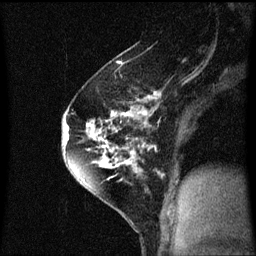
Breast MRI (dynamic contrast-enhanced), one sagittal slice; position 38 of 60 along the scan axis; dynamic contrast-enhanced series, image 2 of 3 at this slice position (ordered by acquisition); 1.5 T; TE 4.2 ms, TR 8.4 ms; 2 mm slice thickness; 256 × 256 image matrix, field of view 200 × 200 mm. Female patient, age 60 years.
Annotated regions visible in this slice (semi-automatic segmentation, software-assisted and operator-edited):
- analysis volume of interest (the breast-tissue region the enhancement analysis was run in; not a lesion): bounding box (x1, y1, x2, y2) in pixels: (64, 70, 147, 195)
- tumour enhancement mask (voxels above the 70 % enhancement threshold inside the analysis volume of interest): (64, 98, 147, 187)